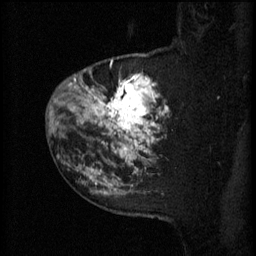
Breast MRI (dynamic contrast-enhanced), one sagittal slice; slice 47 of 60 in the series (ordered by position); 3 images stored at this slice position (order not interpretable as contrast timing); 1.5 T; TE 4.2 ms, TR 11 ms; 2 mm slice thickness; 256 × 256 image matrix. Female patient, age 52 years.
Outlined on this slice (semi-automatic segmentation, software-assisted and operator-edited):
- analysis volume of interest (the breast-tissue region the enhancement analysis was run in; not a lesion): box from (x=81, y=54) to (x=170, y=157) px
- tumour enhancement mask (voxels above the 70 % enhancement threshold inside the analysis volume of interest): (x=81, y=60)–(x=170, y=157)